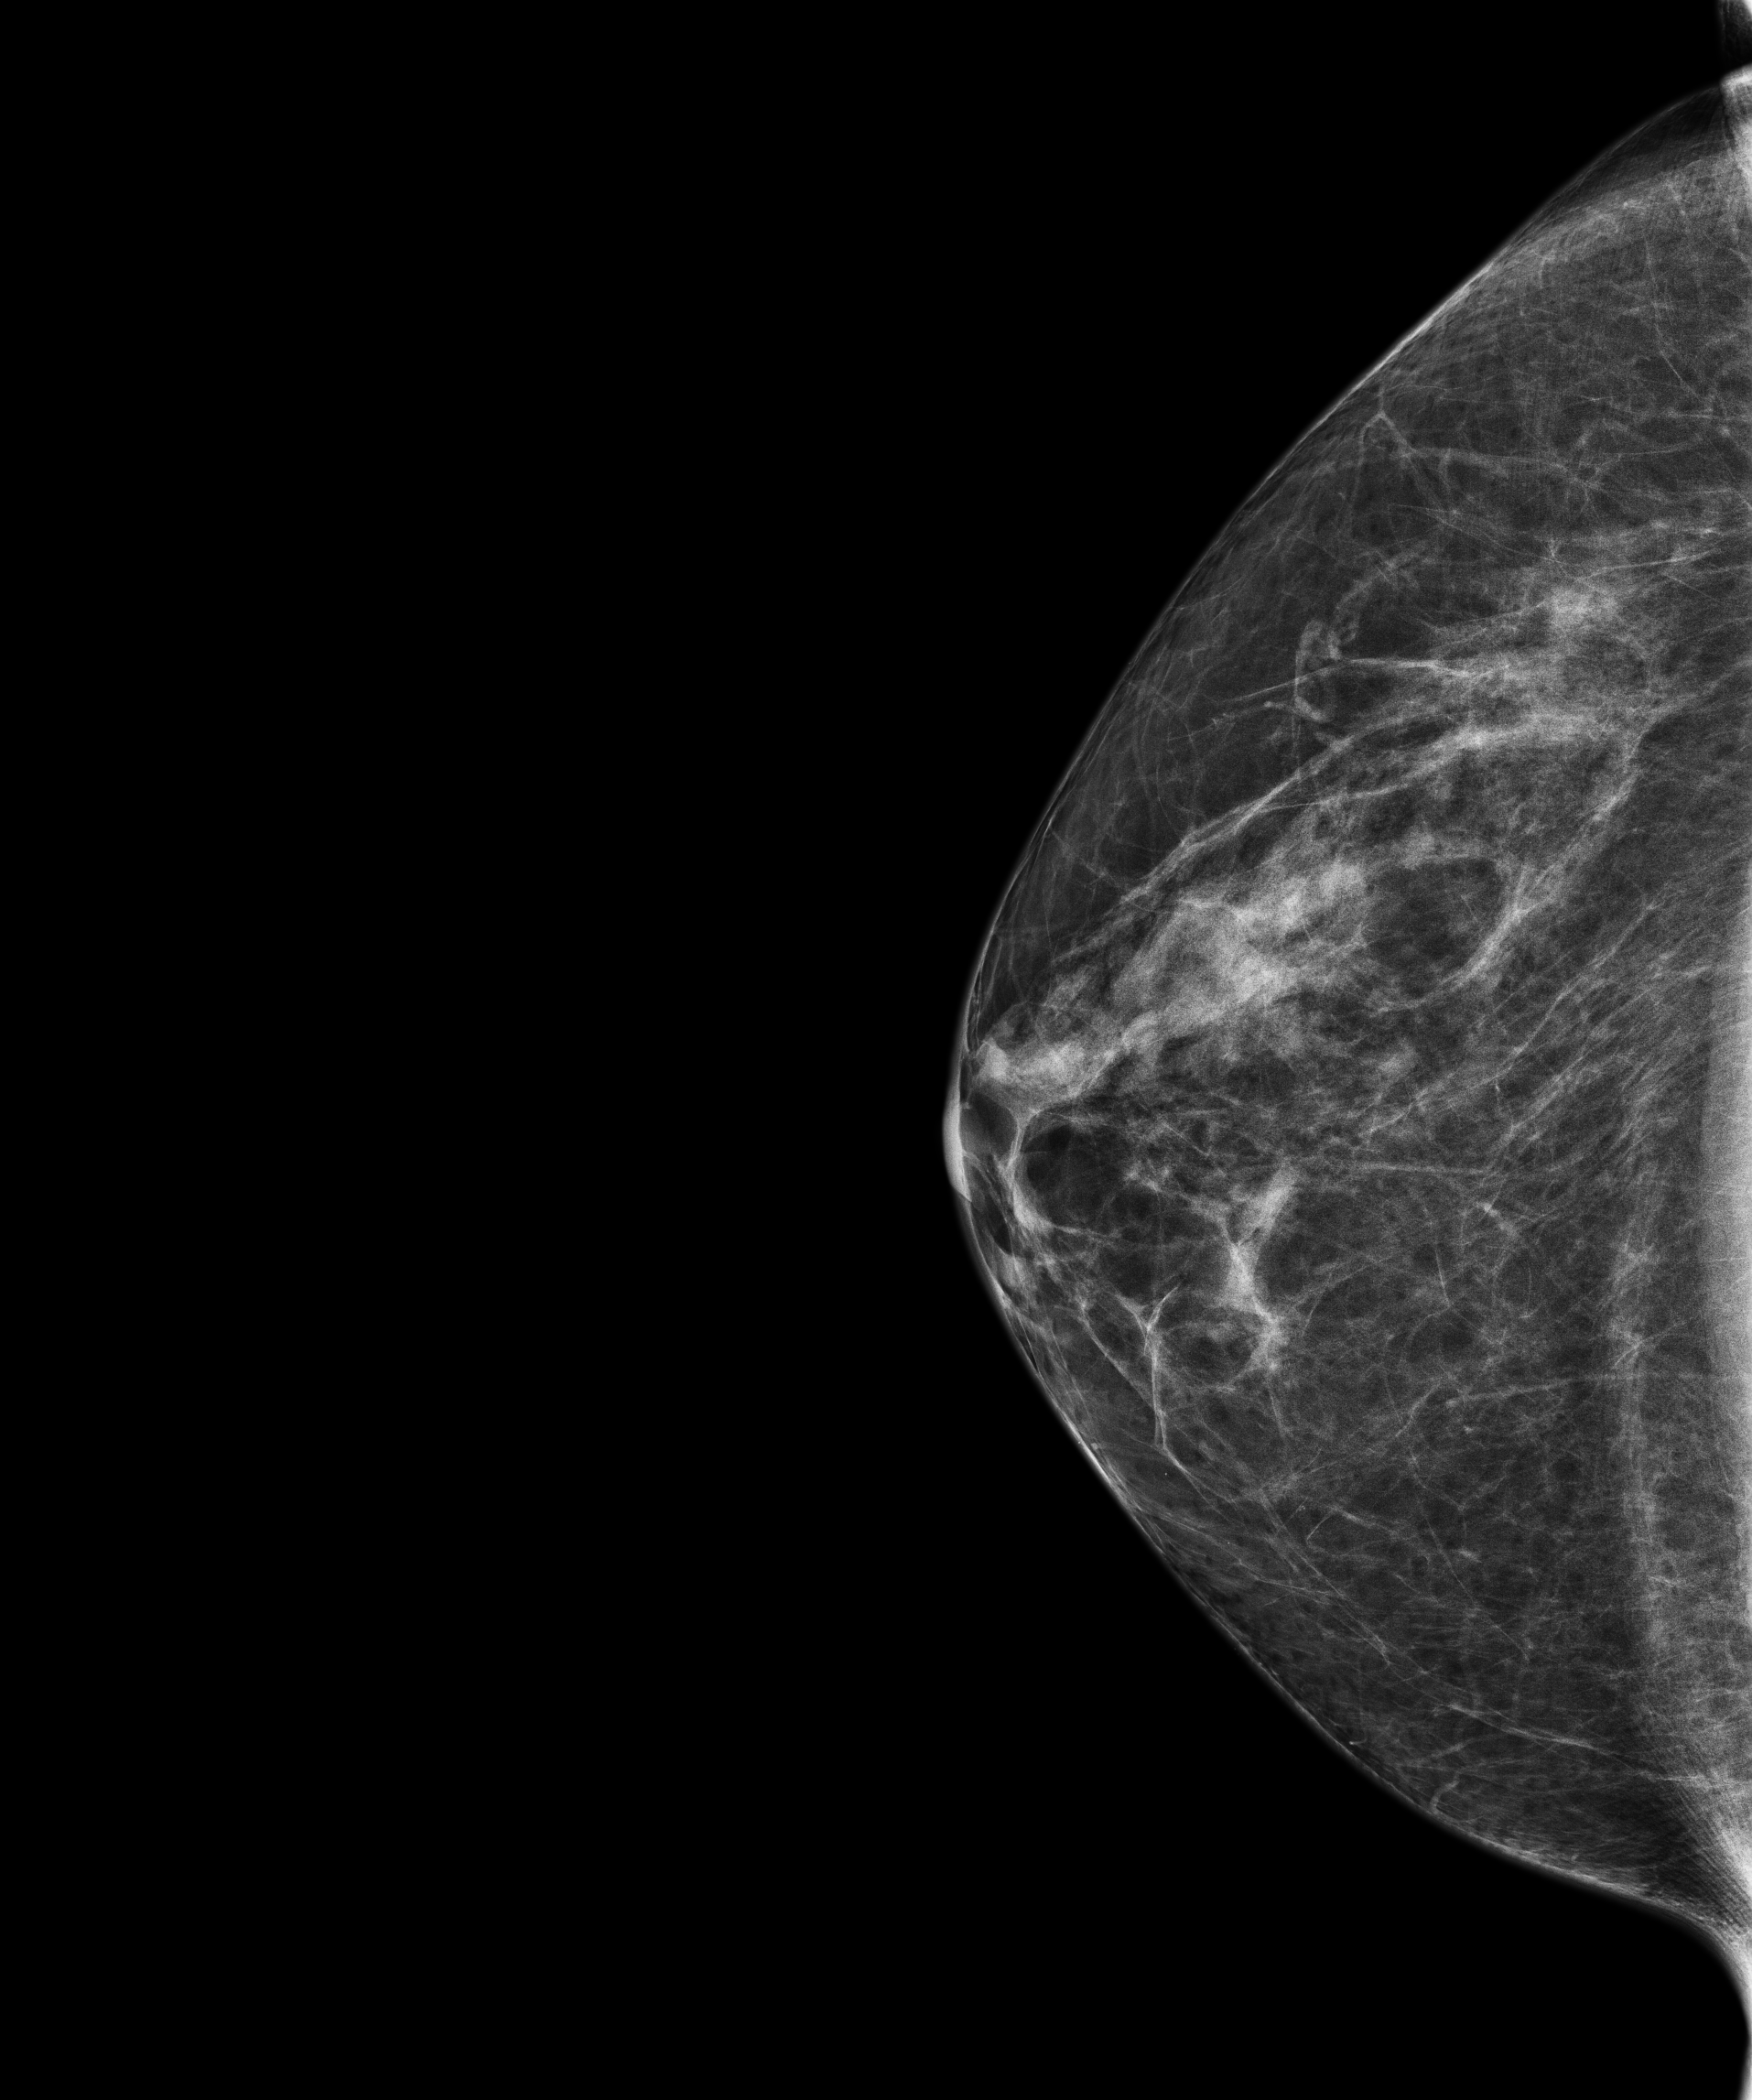
Screening examination, system: Senographe Pristina. Female patient, age 58 years.
Image type: full-field digital mammogram. Breast: right. Projection: CC view.